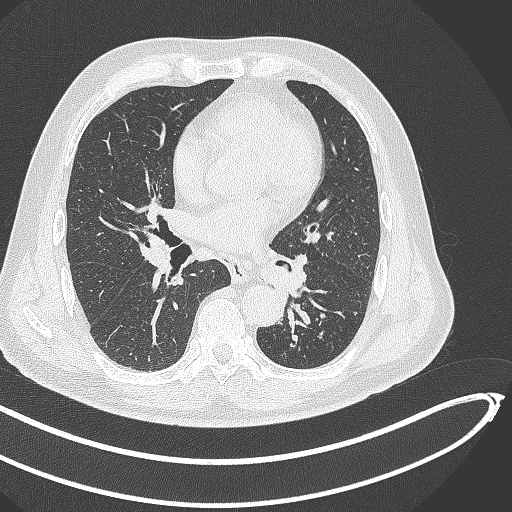
Chest CT, one axial slice; slice 239 of 468 in the series (ordered by position); reconstruction kernel B70f; 120 kVp; lung window (W 1500 / L -600 HU); 1 mm slice thickness; 512 × 512 image matrix, field of view 400 × 400 mm. Patient: male, 64 years. From the clinical record (not read from this slice): clinical TNM (as recorded): T1c N0 M0.
Structures marked on this image (rectangle marked by the reading radiologist):
- lung tumour (recorded histology: squamous cell carcinoma): box from (x=255, y=251) to (x=301, y=303) px